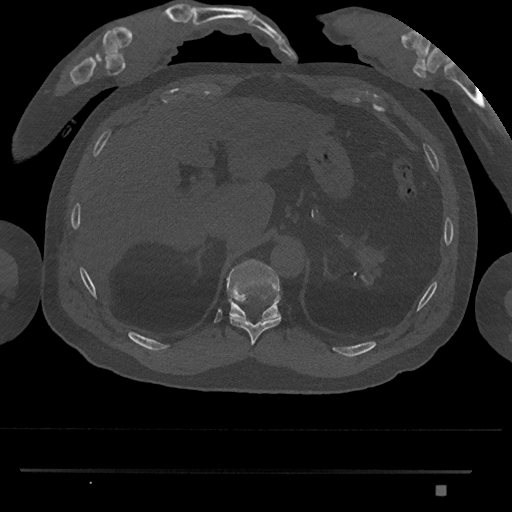
CT including the spine, one axial slice. Slice 978 of 1134 in the series (ordered by position). Bone window (W 1800 / L 400 HU). 512 × 512 image matrix. Male patient, age 65 years. From the clinical record (not read from this slice): primary cancer: prostate.
Outlined on this slice (semi-automatic segmentation, software-assisted and operator-edited):
- T10 vertebra: bounding box <230,317,282,346> (left, top, right, bottom; pixels)
- T11 vertebra: <226,259,281,319>